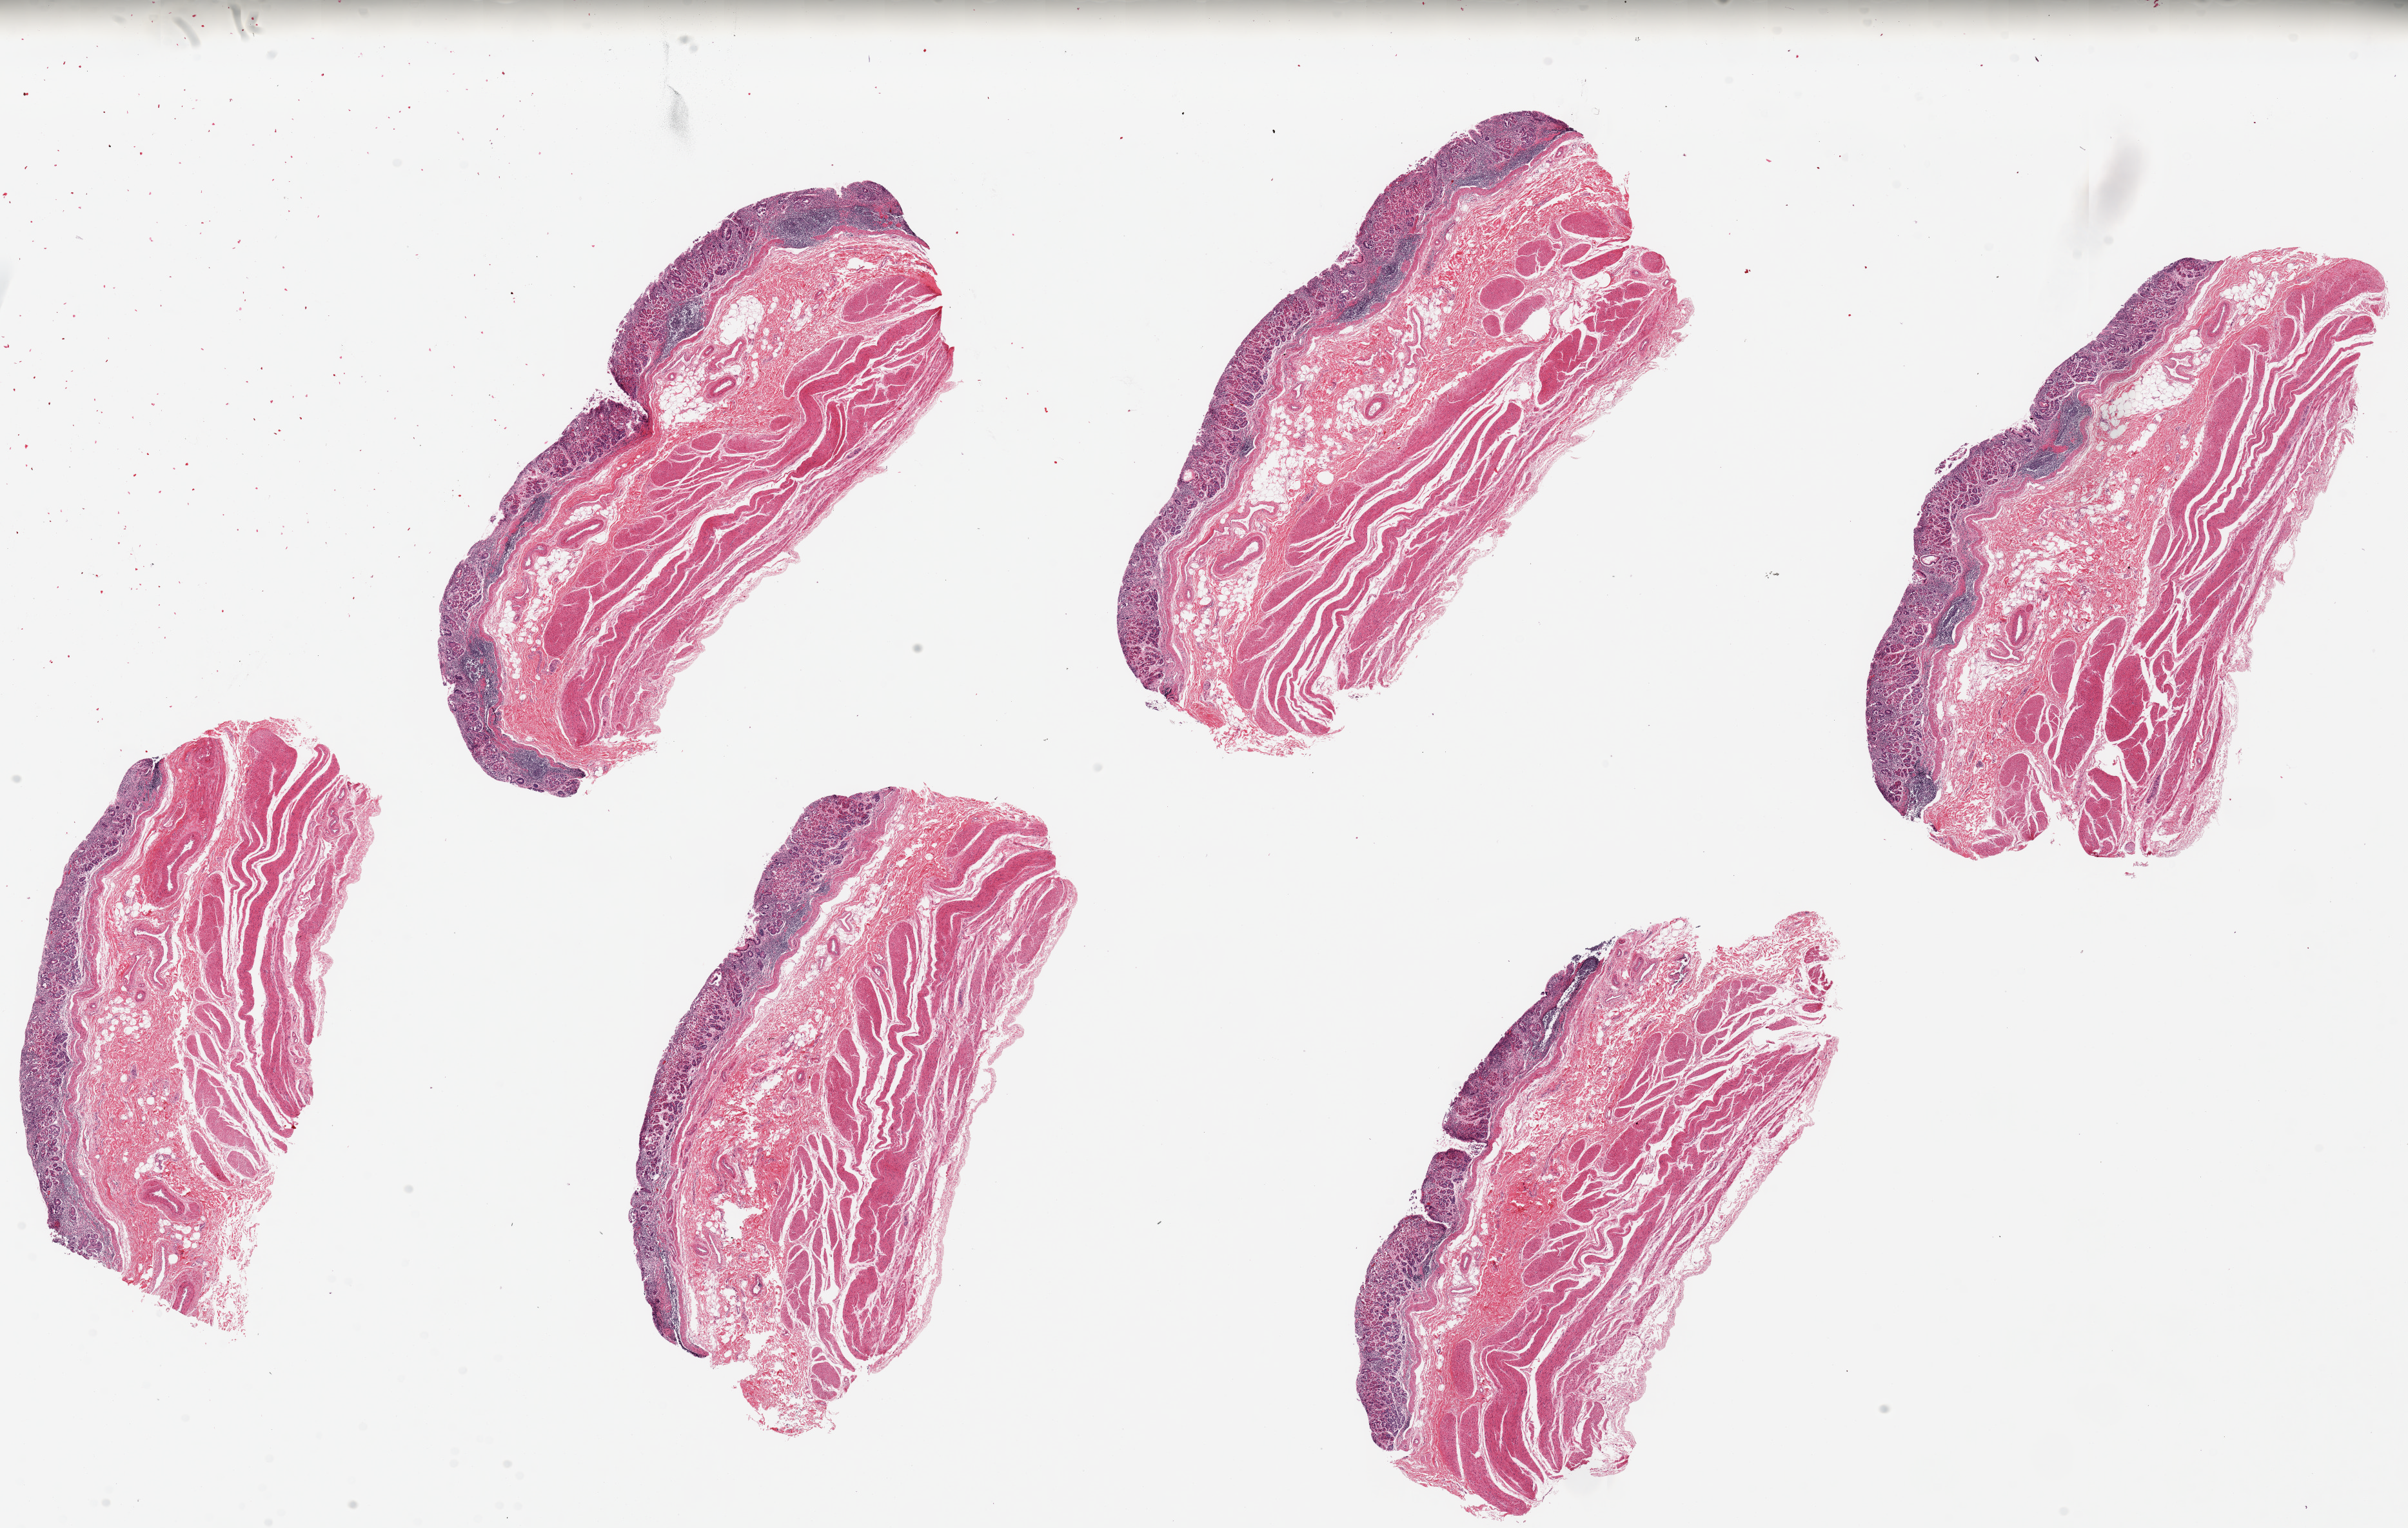
Whole-slide image, haematoxylin and eosin stain, a low-resolution overview of the entire scanned area, about 29.5 x 18.7 mm. PAXgene-fixed paraffin-embedded (PFPE) section. Sampled site (target tissue): stomach. Donor tissue sample. Donor sex: male.
Reviewer comment on this tissue sample: 6 pieces ~8x3mm 10-15% mucosa, moderate-severely autolyzed, diffuse chronic gastritis, pattern suggests H pylori.